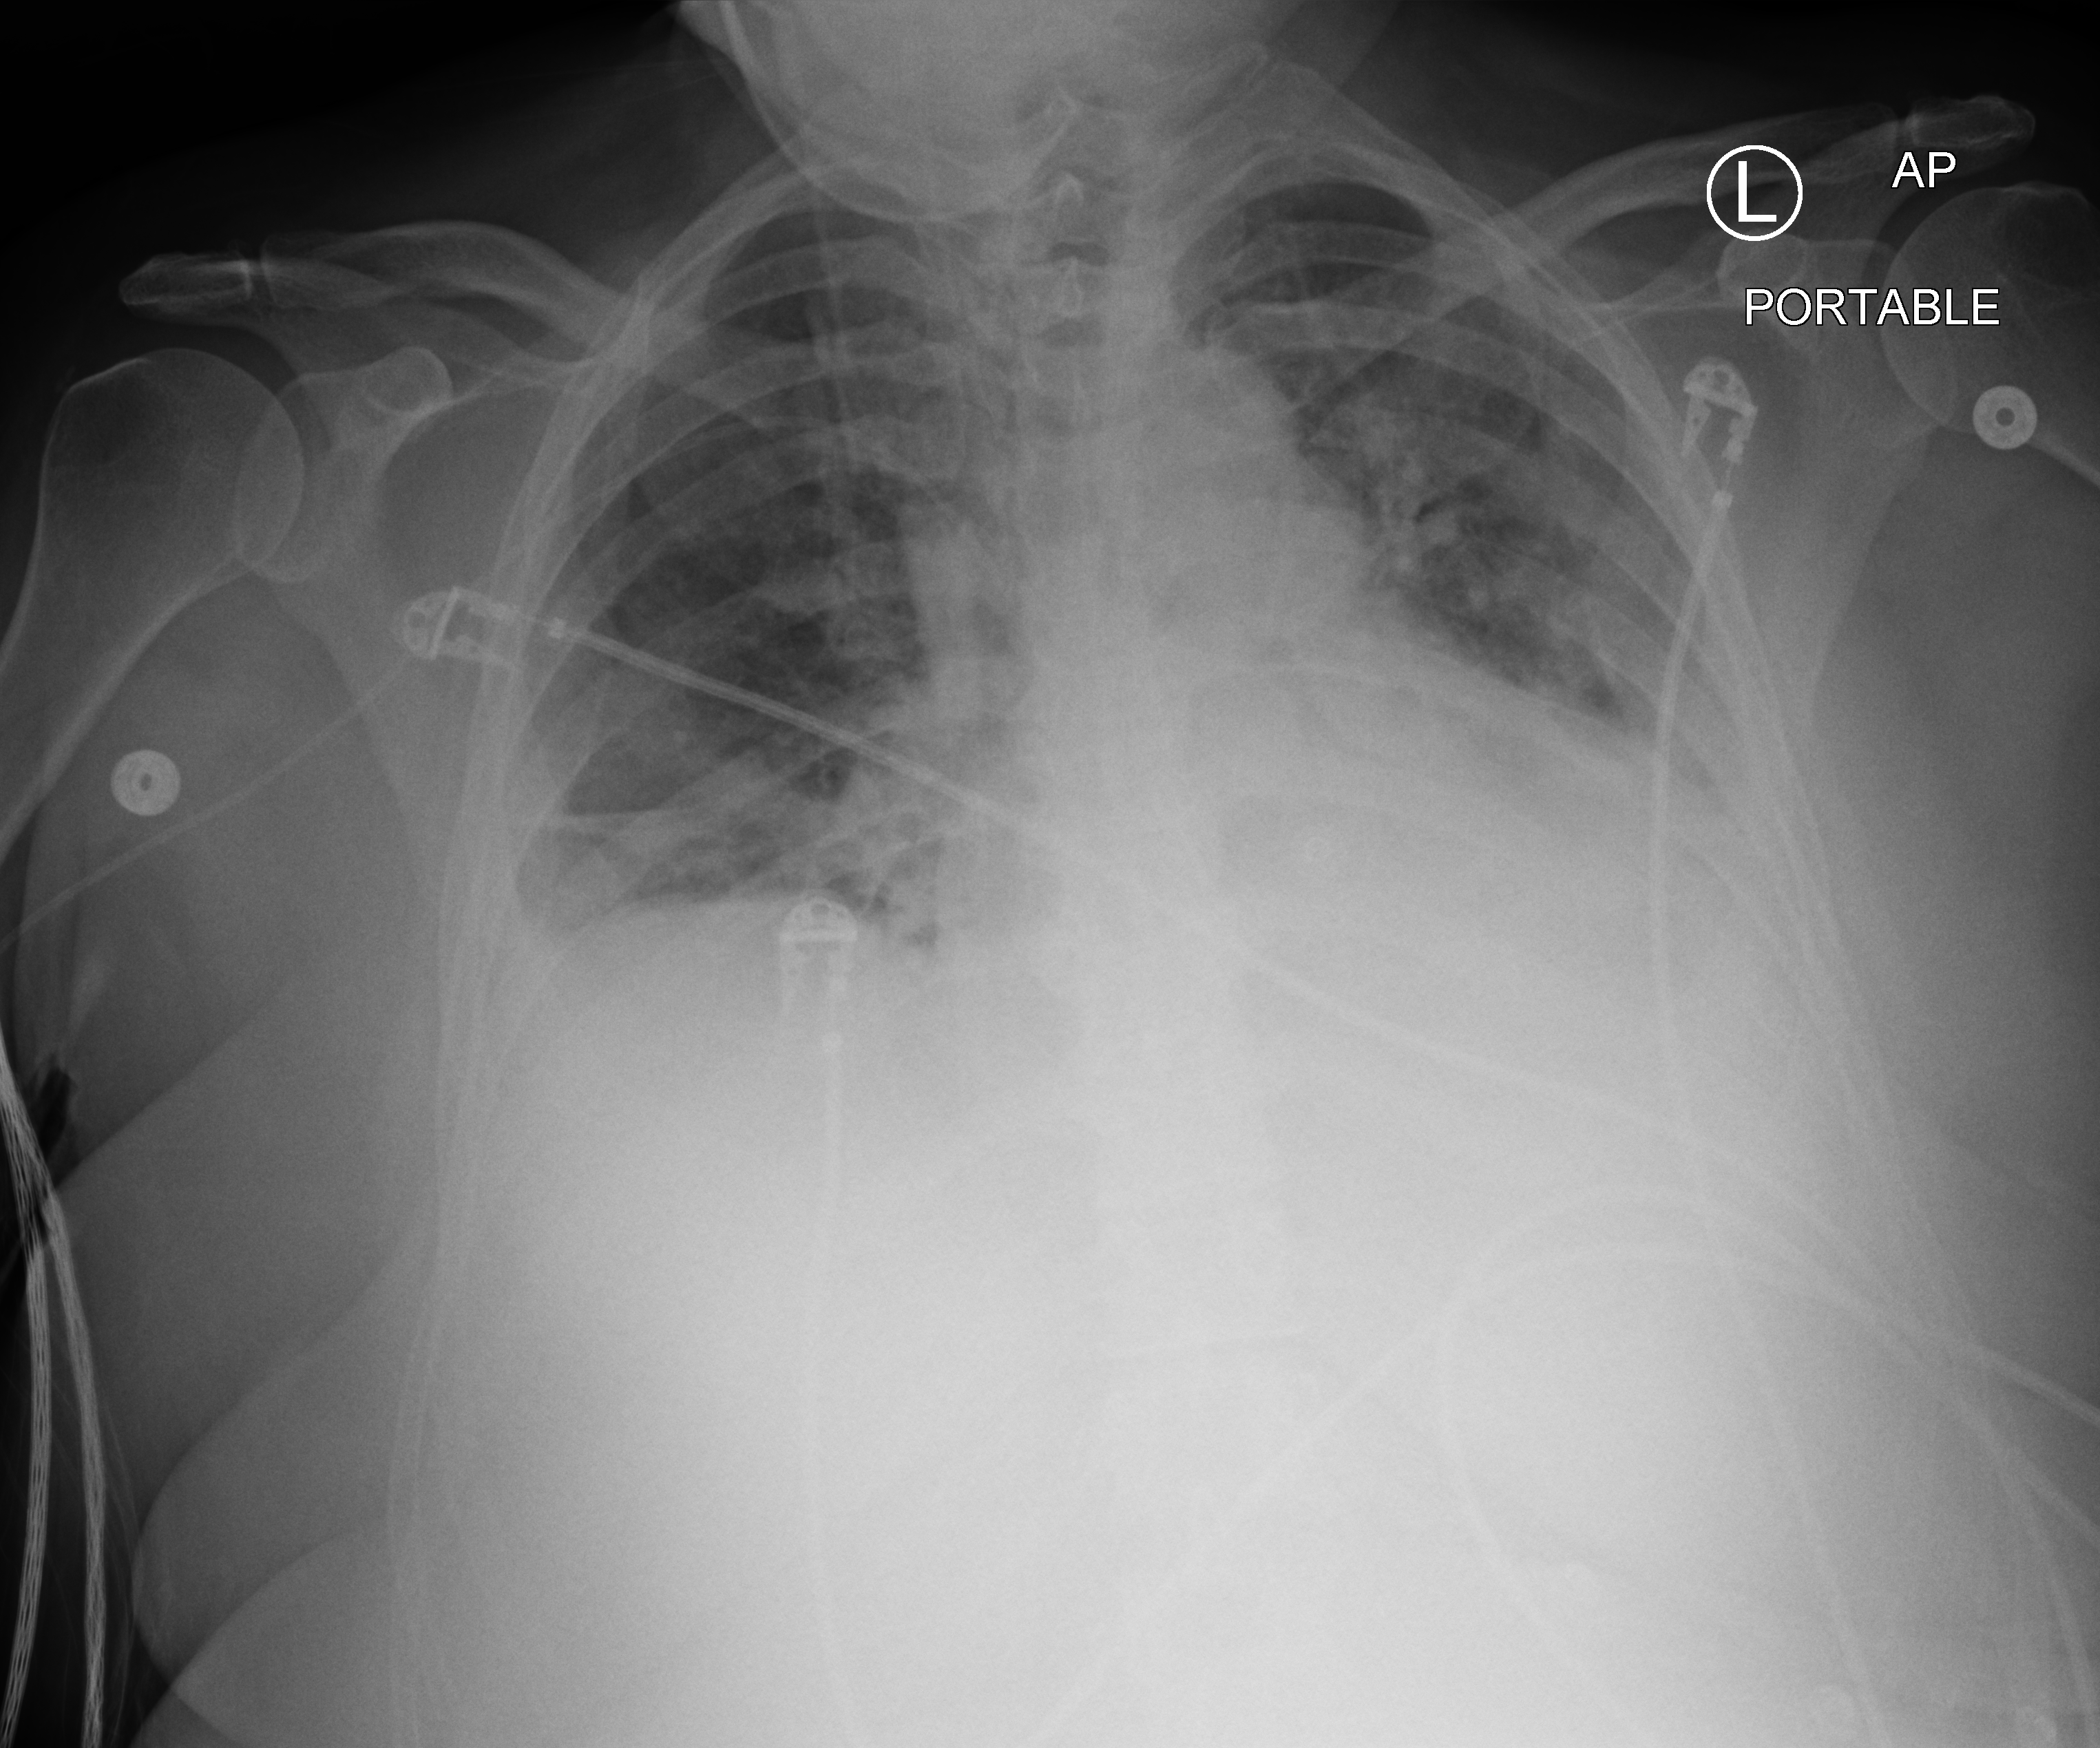
Chest X-ray (portable). Patient hospitalised with COVID-19; female, aged 60–74 years.
Admission-level facts for this patient (not findings on this image; timing relative to this image not recorded):
- admitted to intensive care during this hospital stay: yes
- mechanically ventilated during this hospital stay: yes